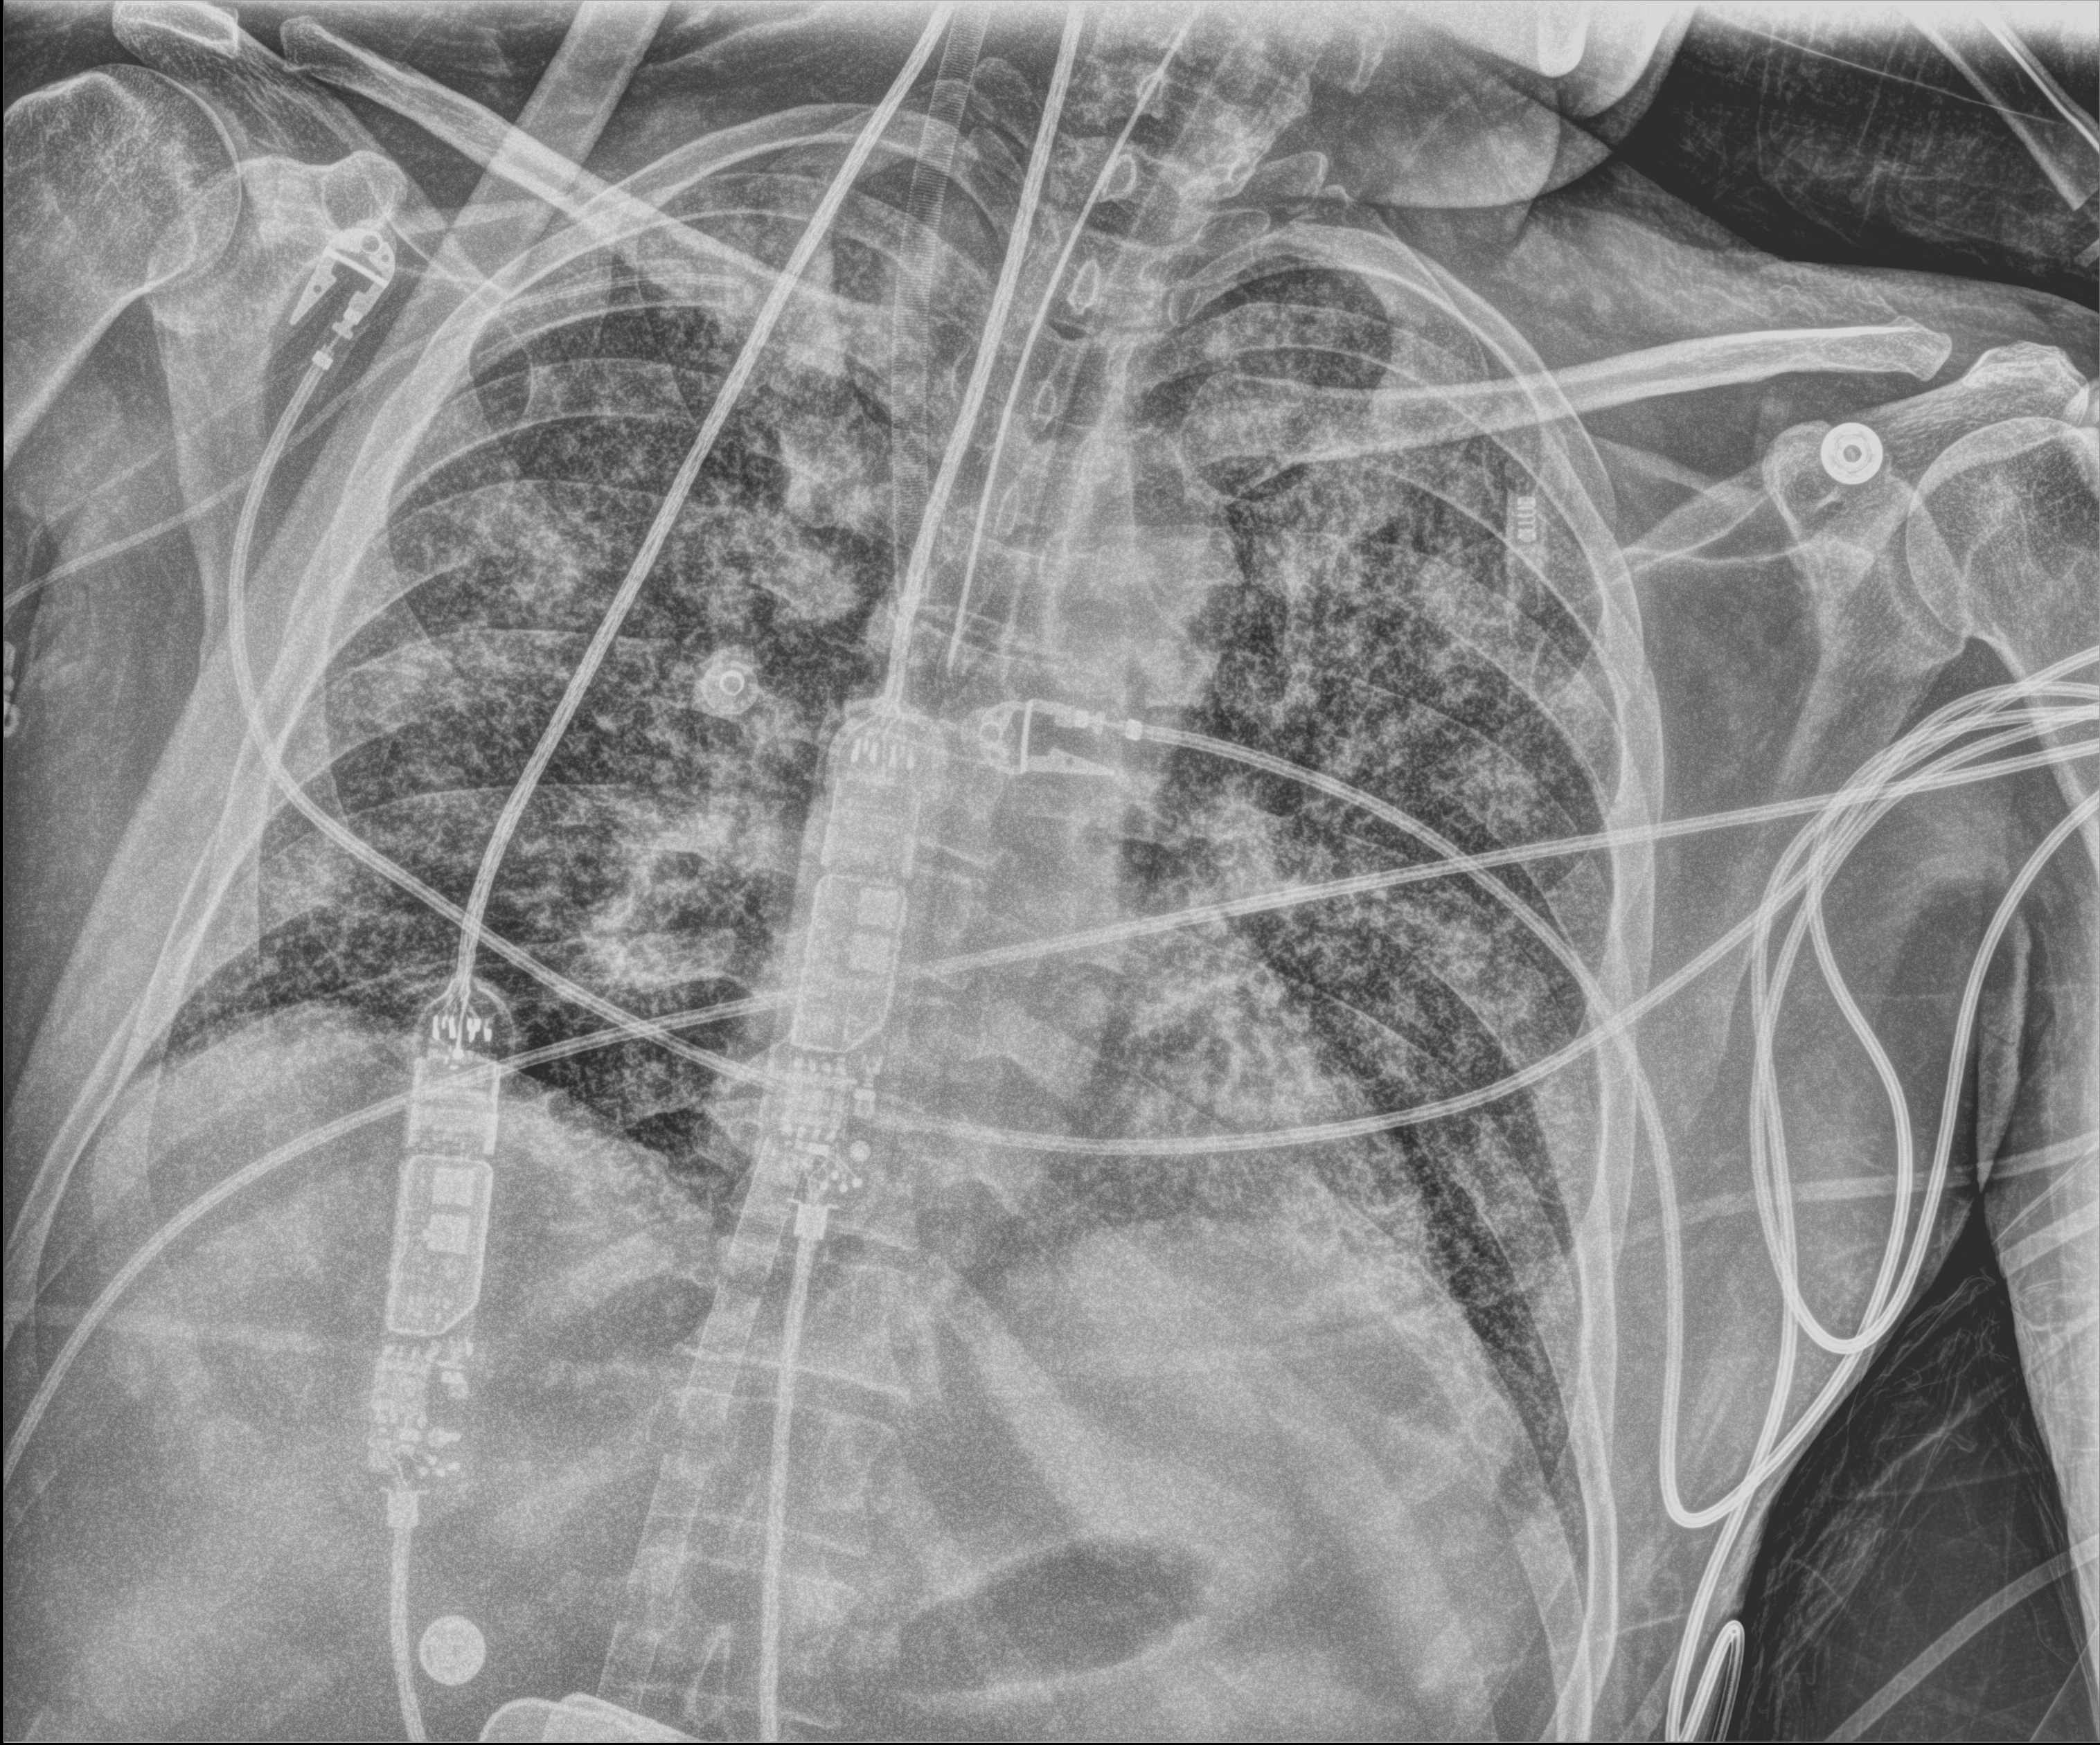
Chest X-ray (portable); anteroposterior (AP) projection. Patient hospitalised with COVID-19; male, aged 18–59 years.
Hospital-stay facts (about this admission, not read from this image; timing relative to this image not recorded): other chronic lung disease (admission record): no; diabetes (admission record): no; admitted to intensive care during this hospital stay: yes.